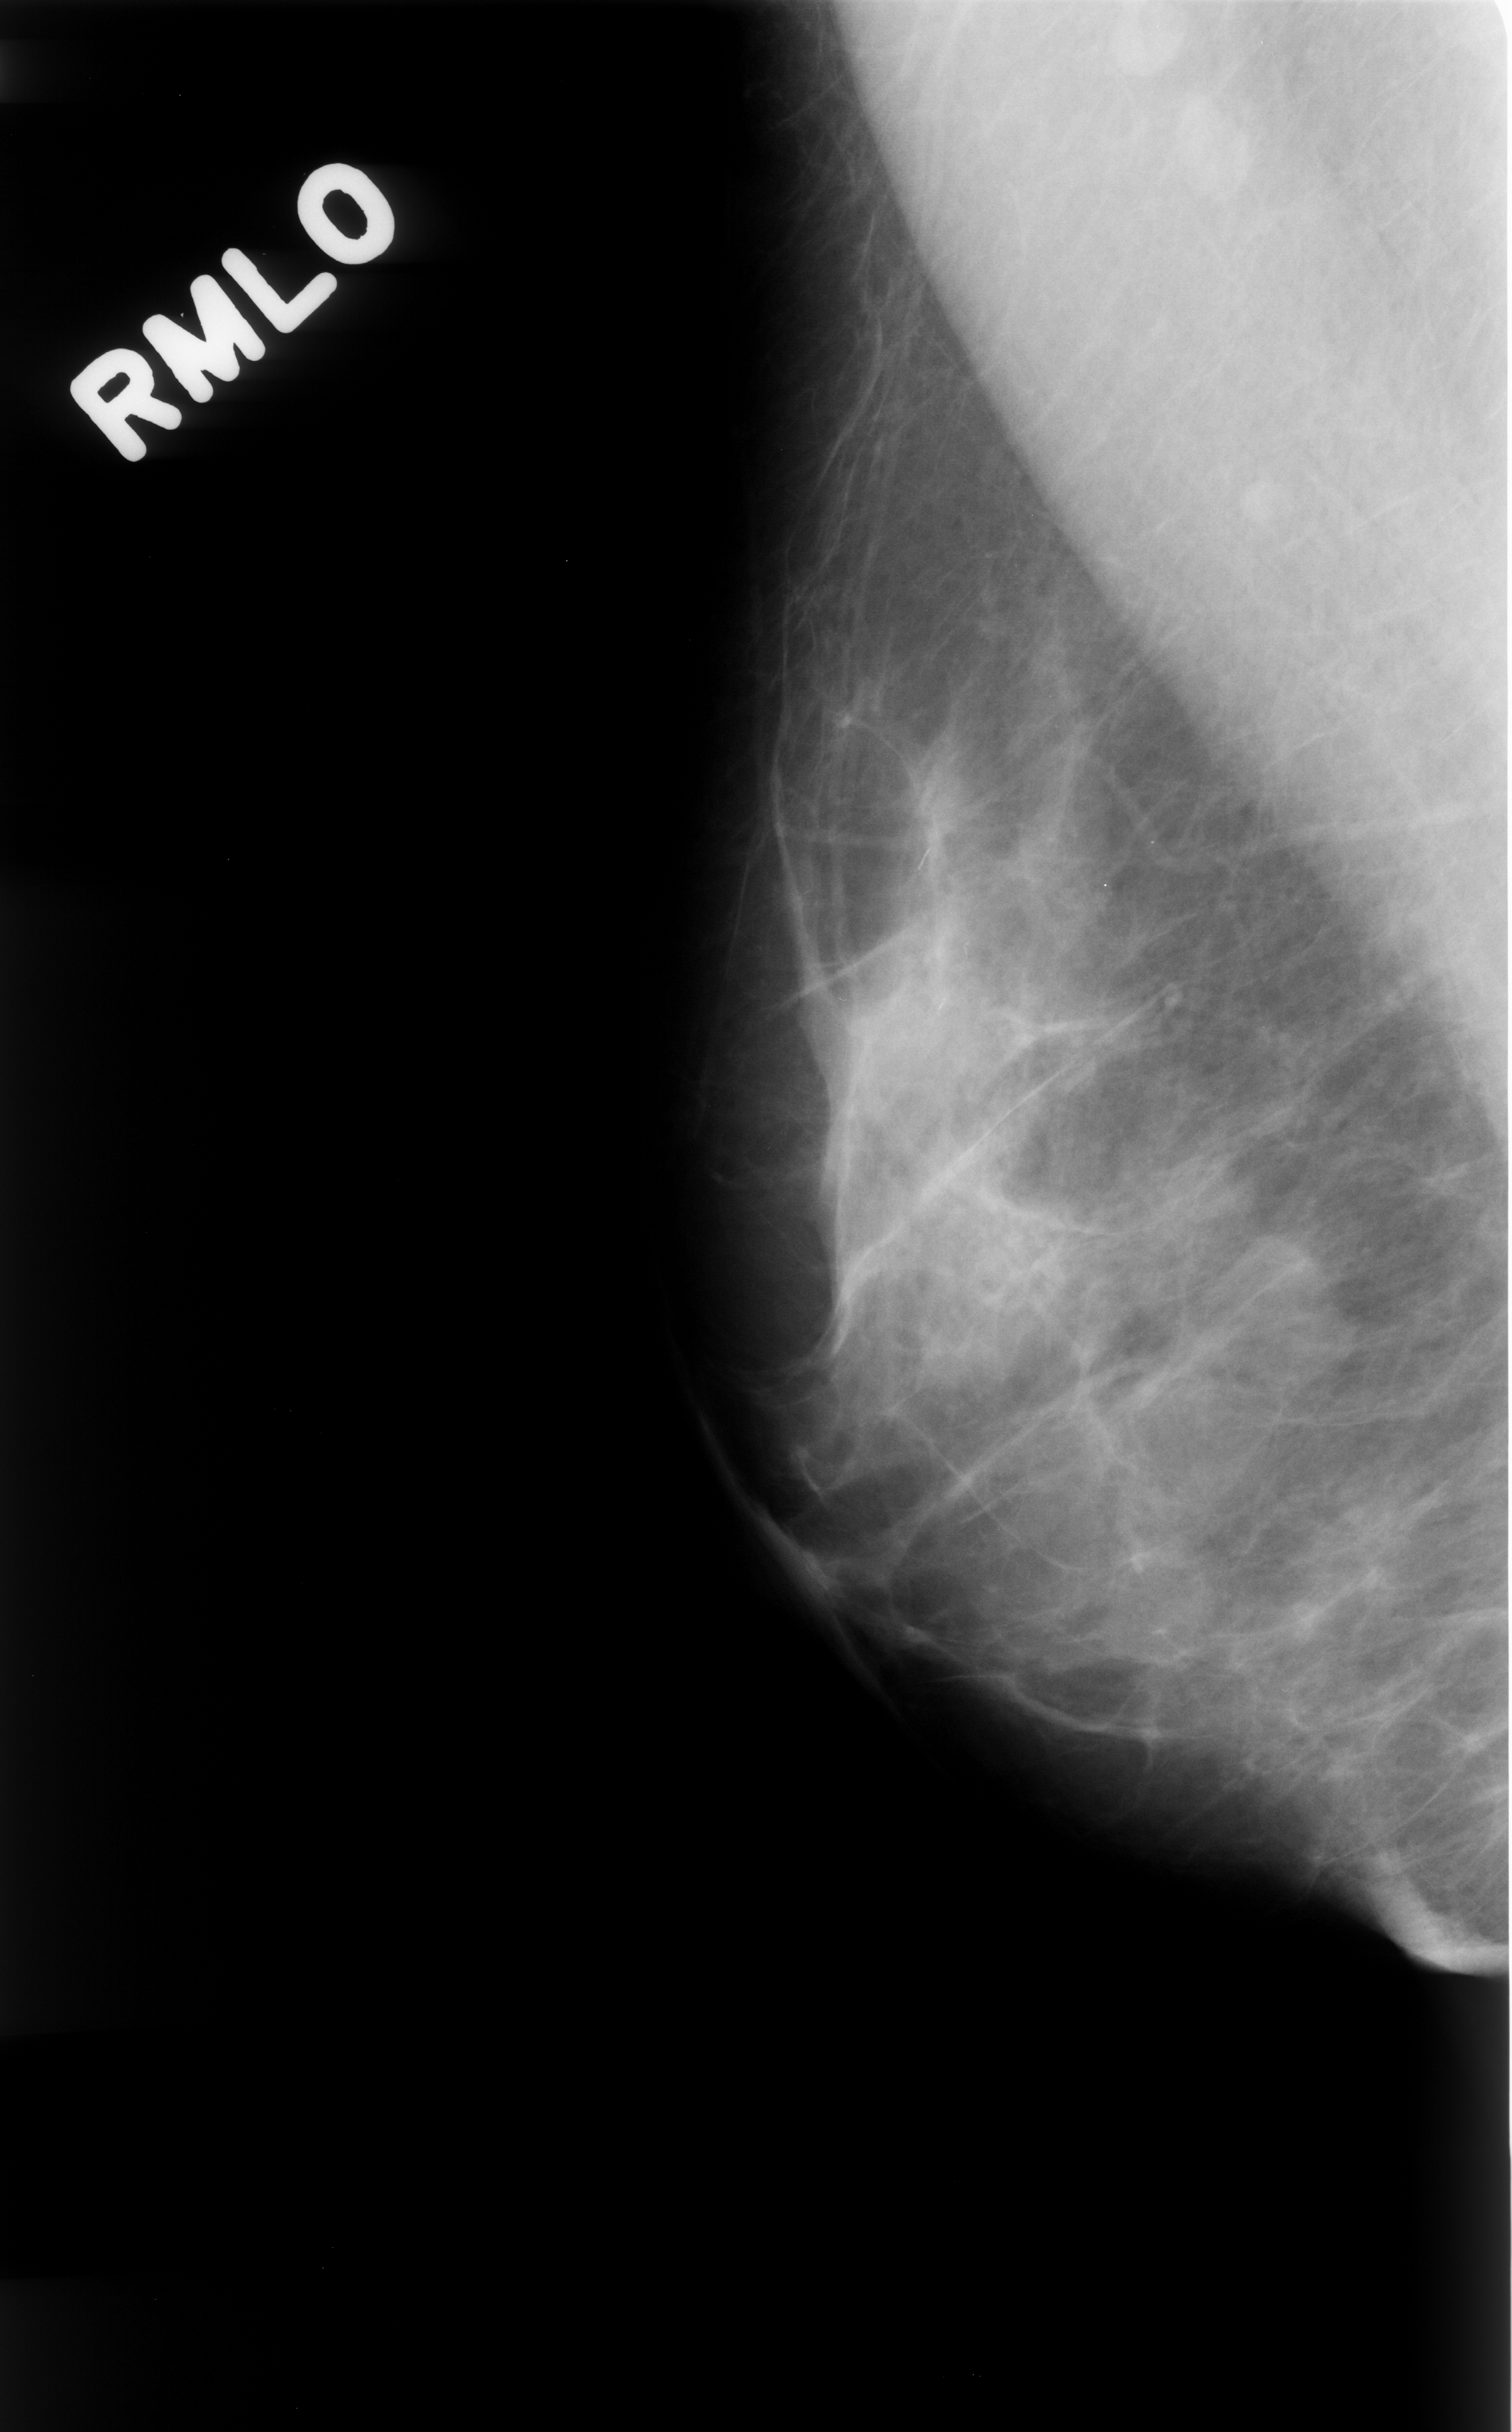
Scanned film-screen mammogram. Right breast. MLO view. BI-RADS breast density category 2 (scale 1–4). 1512 × 2432 image matrix.
Expert-marked regions of interest on this film, with their recorded descriptors:
- calcifications, morphology fine linear branching, distribution linear; BI-RADS assessment category 4; pathology result (as recorded, not read from the image): benign: bounding box (x1, y1, x2, y2) in pixels: (799, 708, 1051, 1116)